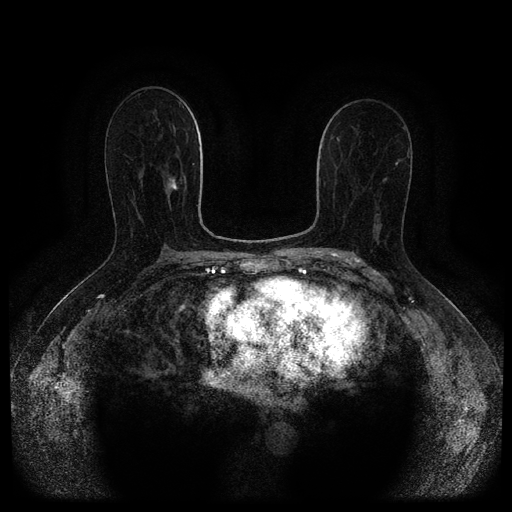
Breast MRI (dynamic contrast-enhanced, multi-phase), one axial slice; position 58 of 116 along the scan axis; dynamic contrast-enhanced series, time point 2 of 5 at this slice position (early post-contrast); 1.5 T; TE 2.7 ms, TR 5.4 ms; 2 mm slice thickness; 512 × 512 image matrix, field of view 340 × 340 mm. Patient: female, 71 years.
Structures marked on this image (semi-automatically segmented with operator editing):
- breast lesion (labelled 'tumour' in the annotation; benign lesions carry a separate 'benign' label): bounding box <168,177,178,190> (left, top, right, bottom; pixels)